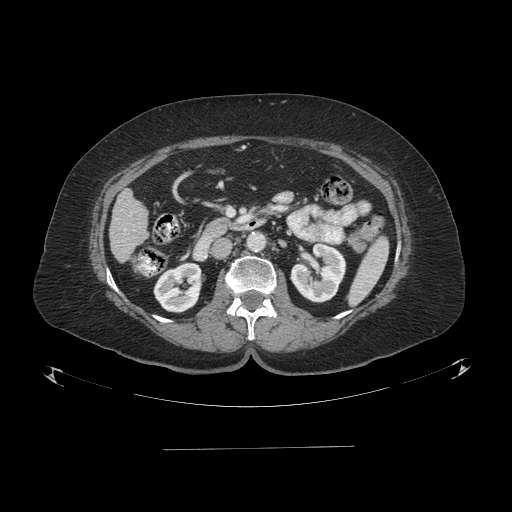
Contrast-enhanced abdominal CT (liver protocol), one axial slice. Slice 26 of 103 in the series (ordered by position). Reconstruction kernel STANDARD. 120 kVp. One of 2 acquisitions stored at this slice position. Soft-tissue window (W 400 / L 40 HU). 2.5 mm slice thickness. 512 × 512 image matrix, field of view 500 × 500 mm. Case-level facts recorded for this patient, not image findings: diagnosis: hepatocellular carcinoma (patient treated with transarterial chemoembolisation; whether this scan precedes or follows treatment is not stated here); TNM stage (as recorded): Stage-IIIA.
Structures marked on this image (semi-automatic segmentation, software-assisted and operator-edited):
- liver parenchyma outside the tumour (the mass and vessels are separate outlines, so this box may not span the whole liver): box from (x=108, y=189) to (x=148, y=262) px